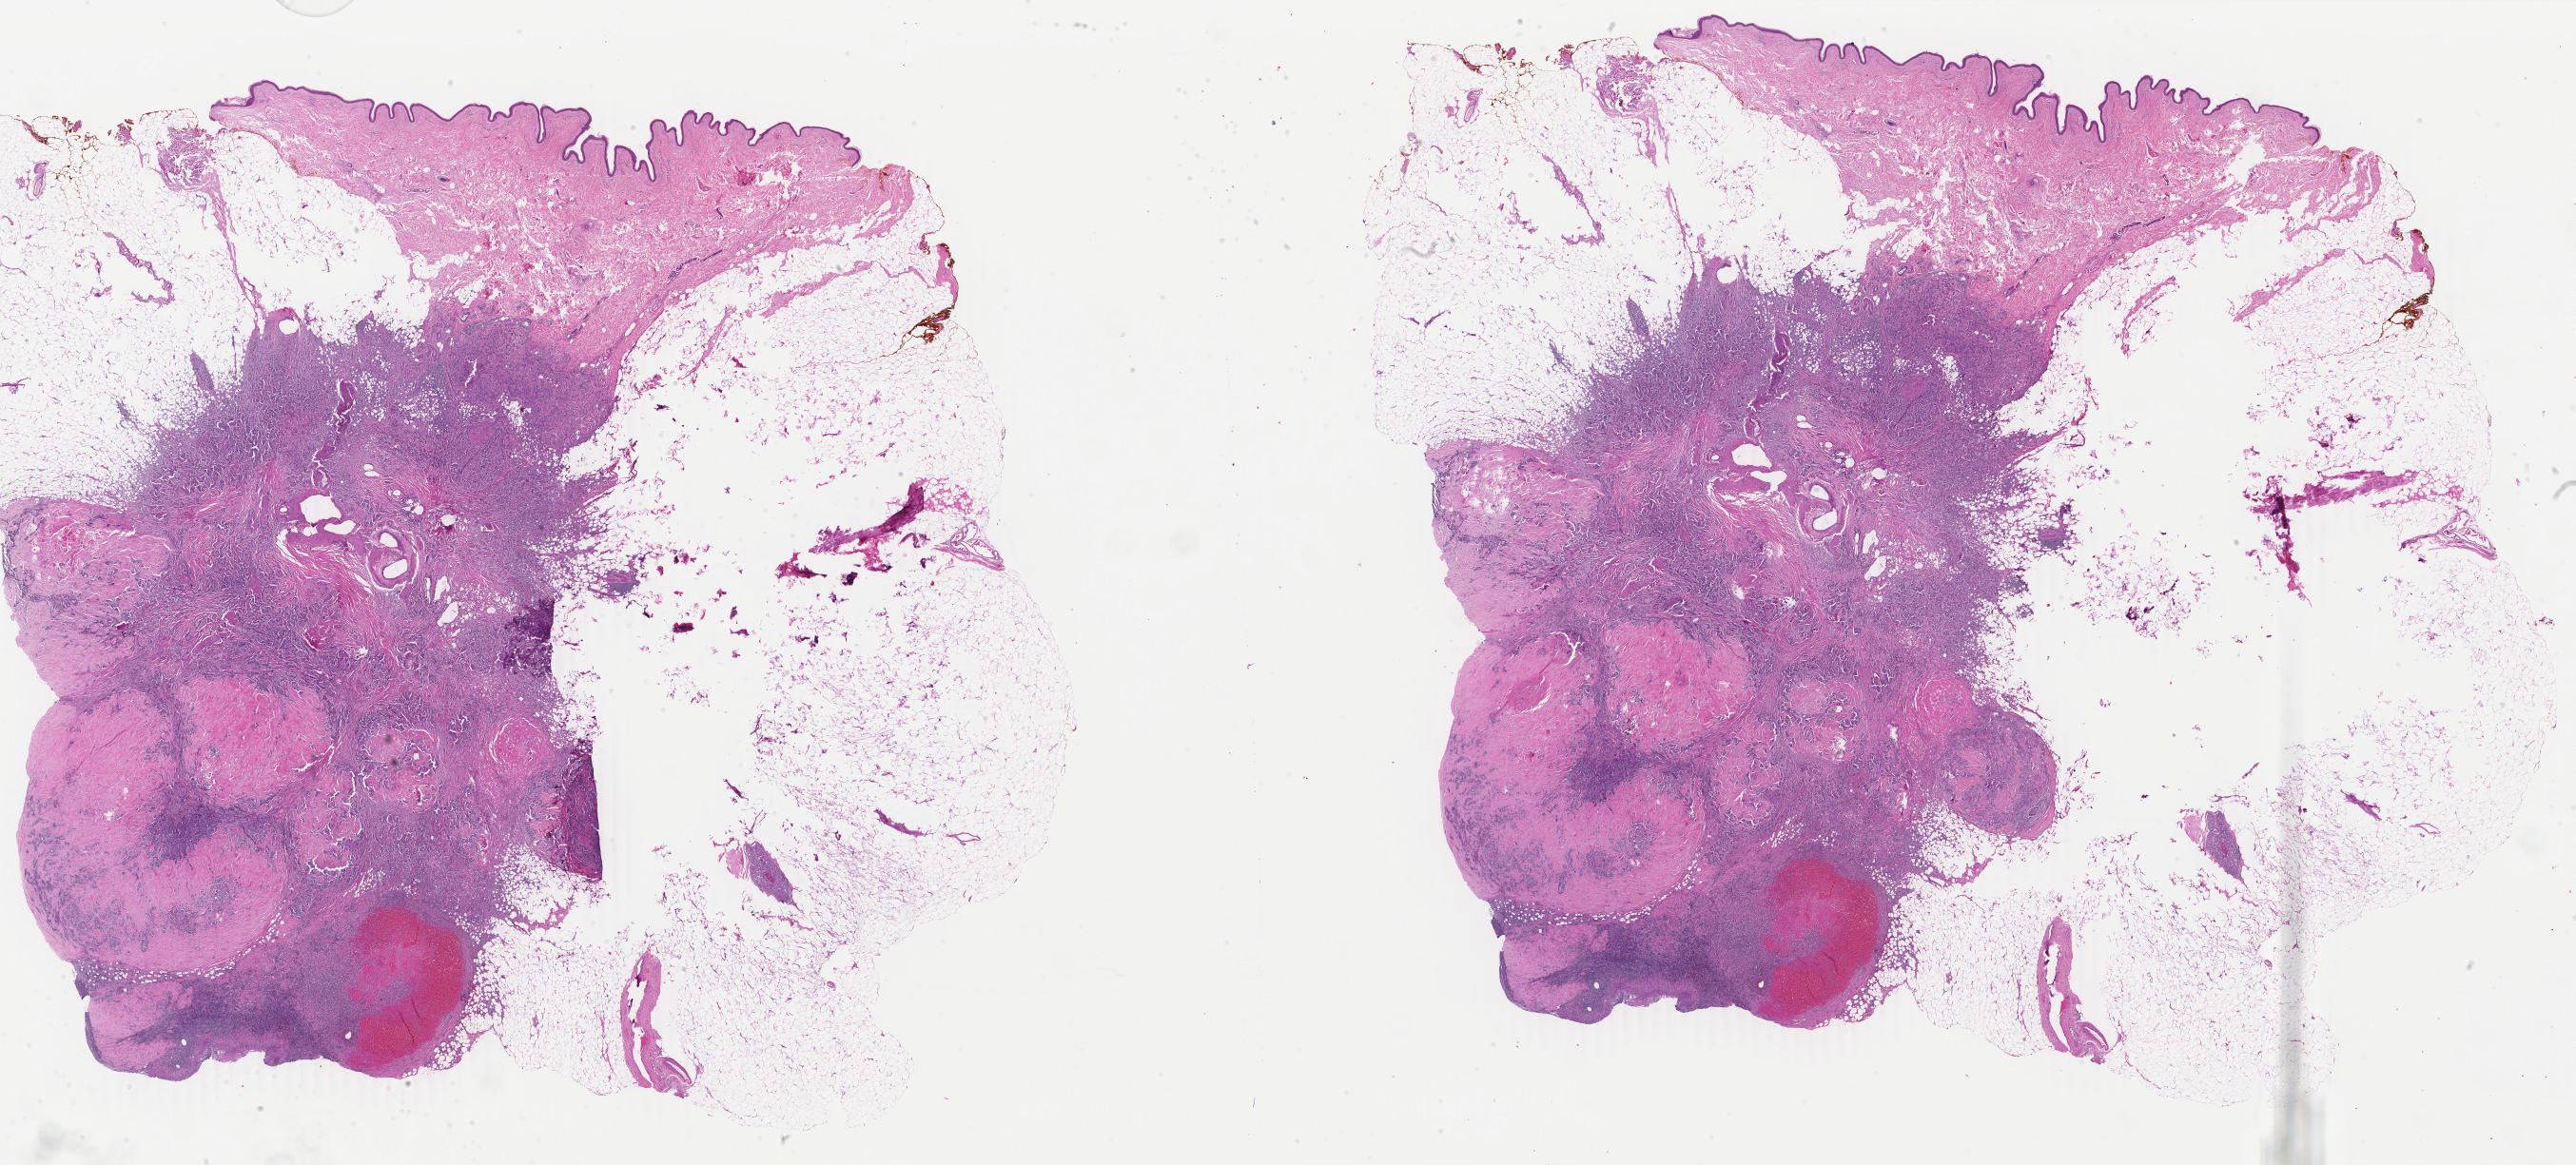
Digitized Hematoxylin and eosin (H&E) stained tissue section (whole slide), whole scanned area (about 43.1 x 19.5 mm, acquisition: 40x scan) shown as a low-resolution overview, formalin-fixed paraffin-embedded (FFPE) diagnostic section, primary tumour sample from the breast. Female patient; age at initial diagnosis 80 years.
Diagnosis: Infiltrating duct carcinoma, NOS.